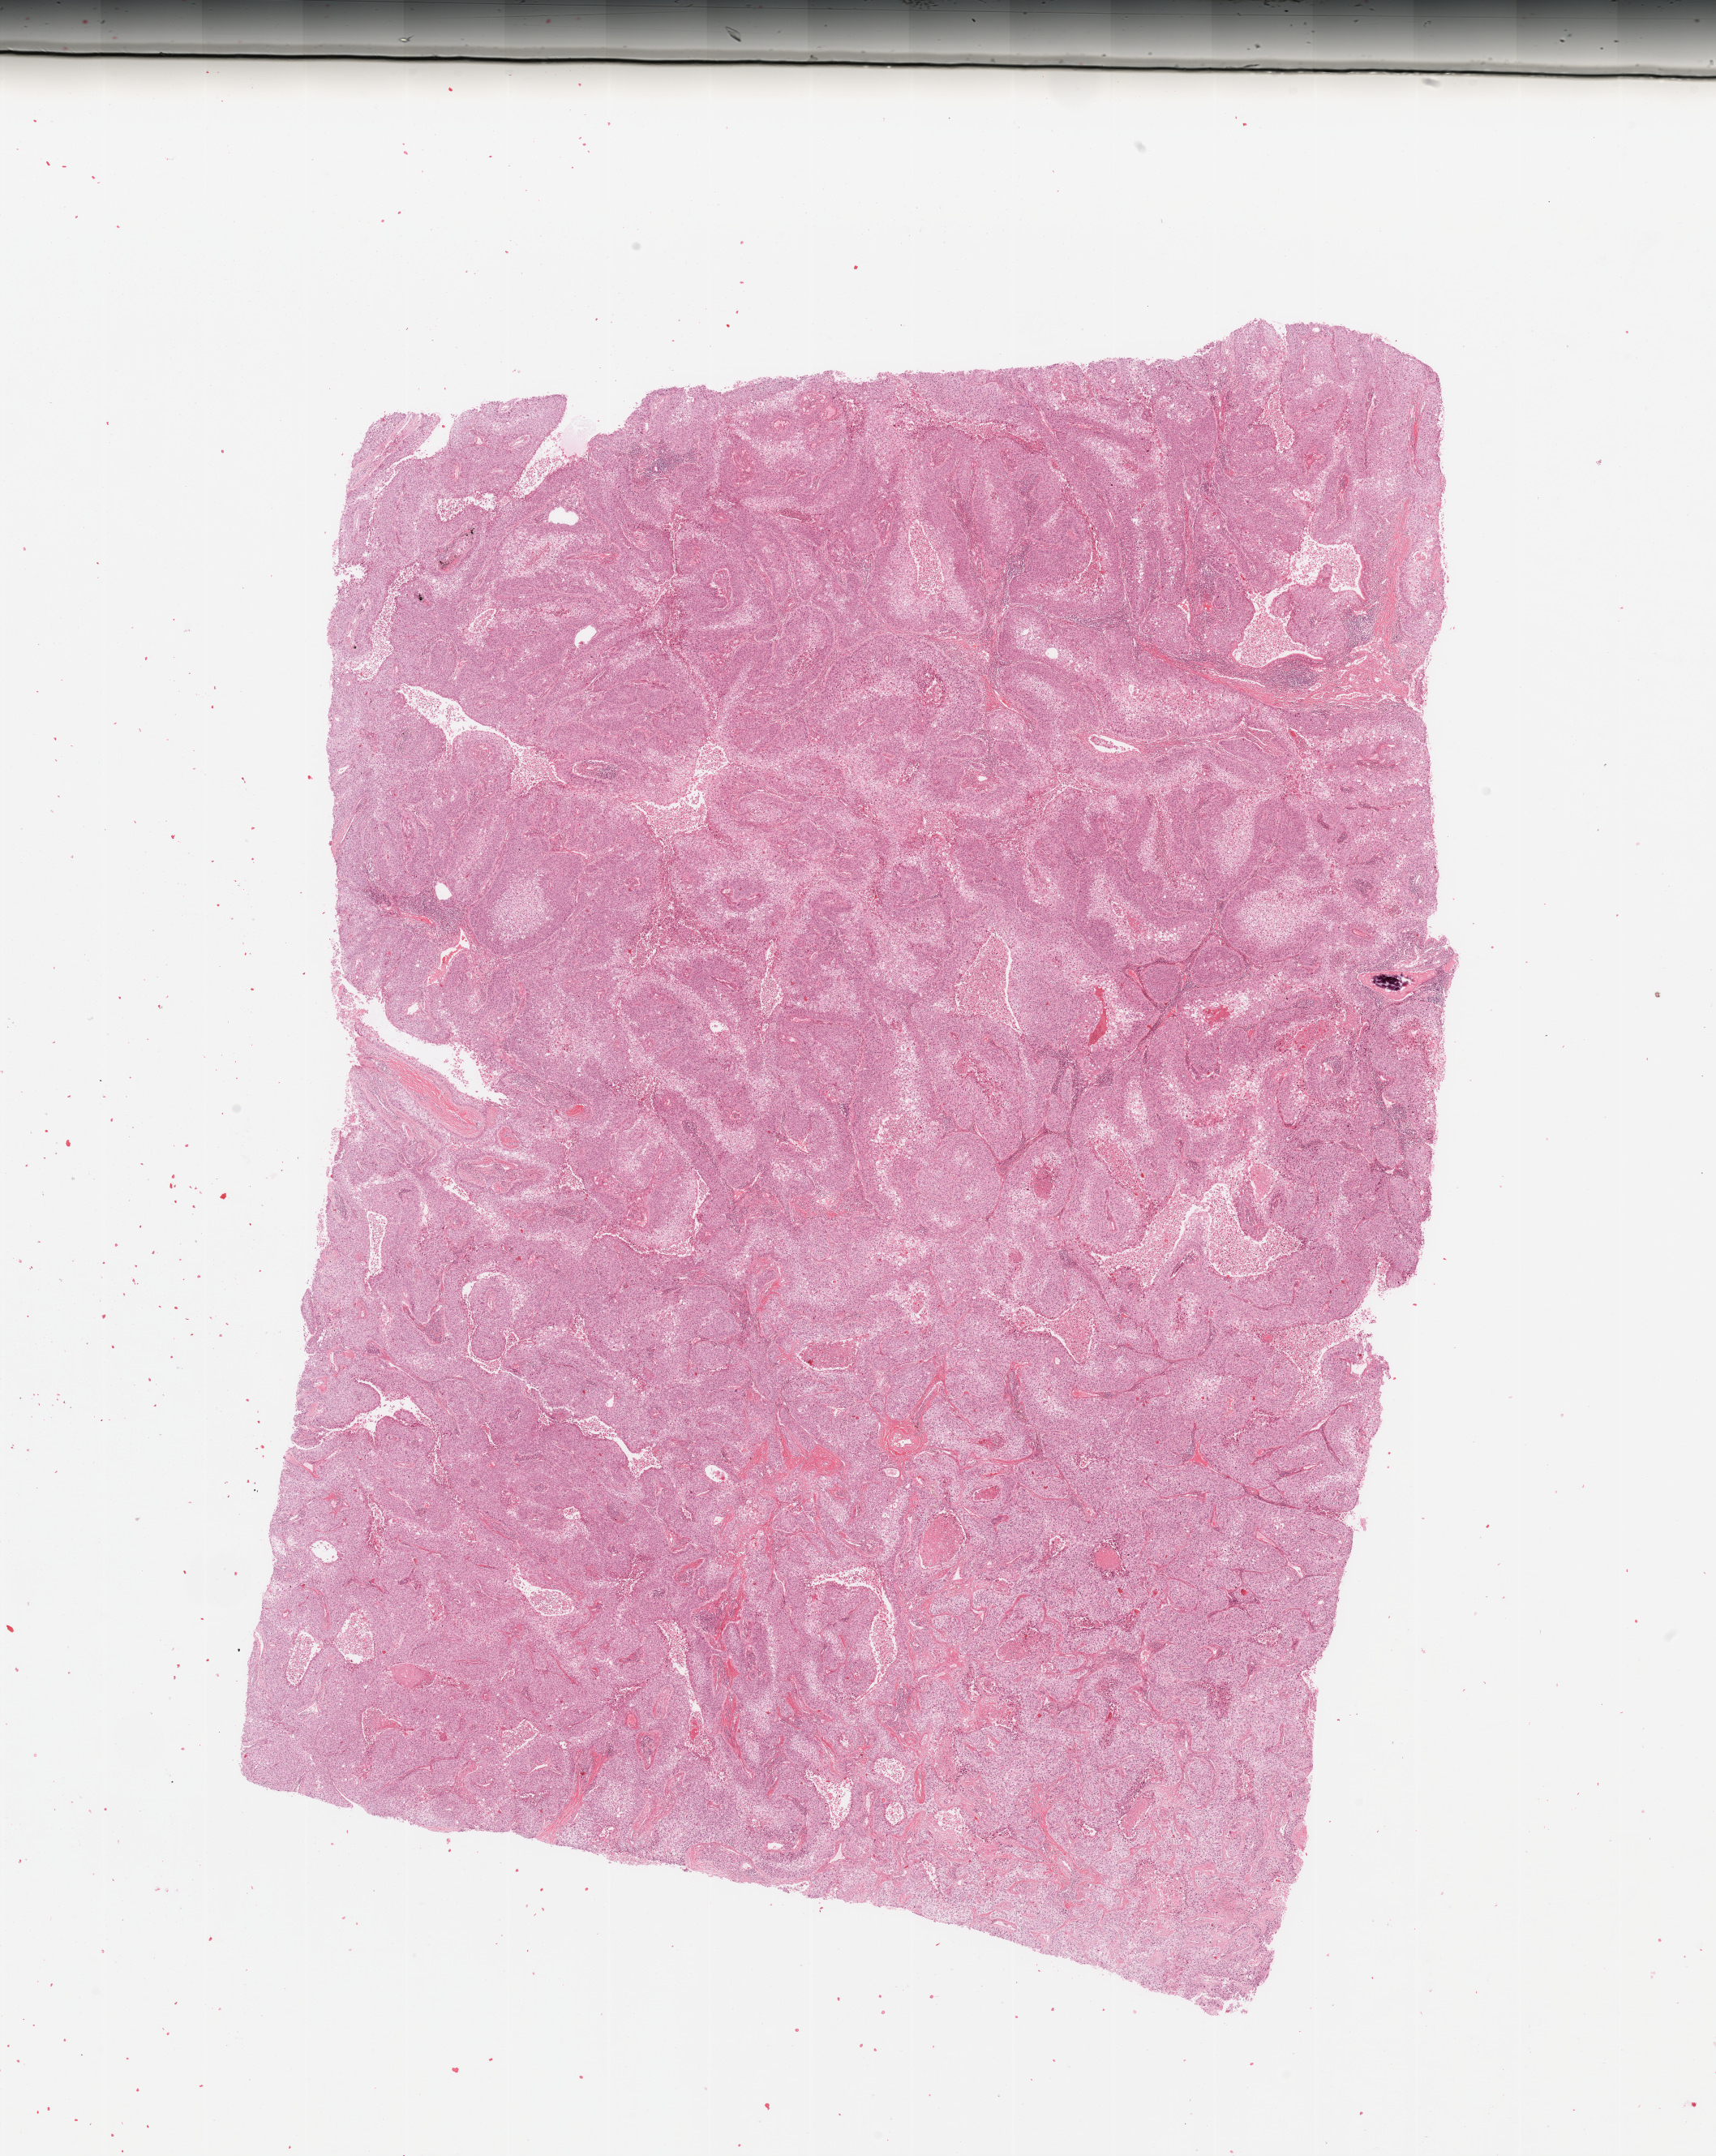
Whole-slide histology image, Hematoxylin and eosin (H&E) stained — whole scanned area (about 16.7 x 21.0 mm) shown as a low-resolution overview; lung, tumour tissue. Patient: male, age 59 years. Histologic grade: G2 (moderately differentiated).
Diagnosis: Squamous cell carcinoma, NOS. AJCC pathologic stage: IIB.